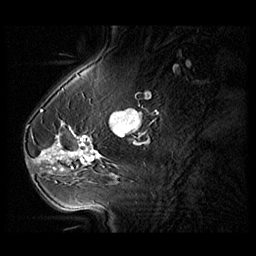
Breast MRI (dynamic contrast-enhanced), one sagittal slice; position 34 of 104 along the scan axis; 3 images stored at this slice position (order not interpretable as contrast timing); 1.5 T; TE 1.3 ms, TR 5.5 ms; 3 mm slice thickness; 256 × 256 image matrix, field of view 220 × 220 mm. Female patient, age 54 years. From the clinical record (not read from this slice): setting: breast cancer imaged before/during neoadjuvant chemotherapy; receptor status: HR-positive, HER2-negative.
Outlined on this slice (semi-automatically segmented with operator editing):
- analysis volume of interest (the breast-tissue region the enhancement analysis was run in; not a lesion): box from (x=28, y=127) to (x=104, y=182) px
- tumour enhancement mask (voxels above the 140 % enhancement threshold inside the analysis volume of interest): (x=36, y=135)–(x=98, y=170)